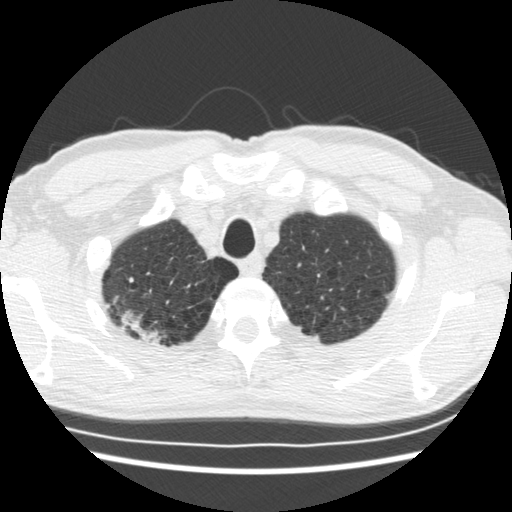
Low-dose screening chest CT, one axial slice. Position 158 of 183 along the scan axis. Reconstruction kernel STANDARD. 120 kVp. Lung window (W 1500 / L -600 HU). 512 × 512 image matrix, field of view 339 × 339 mm.
Outlined on this slice (expert manual segmentation):
- lesion 1 (tumor, upper lobe of right lung): bounding box [x1, y1, x2, y2] px = [123, 312, 163, 344]